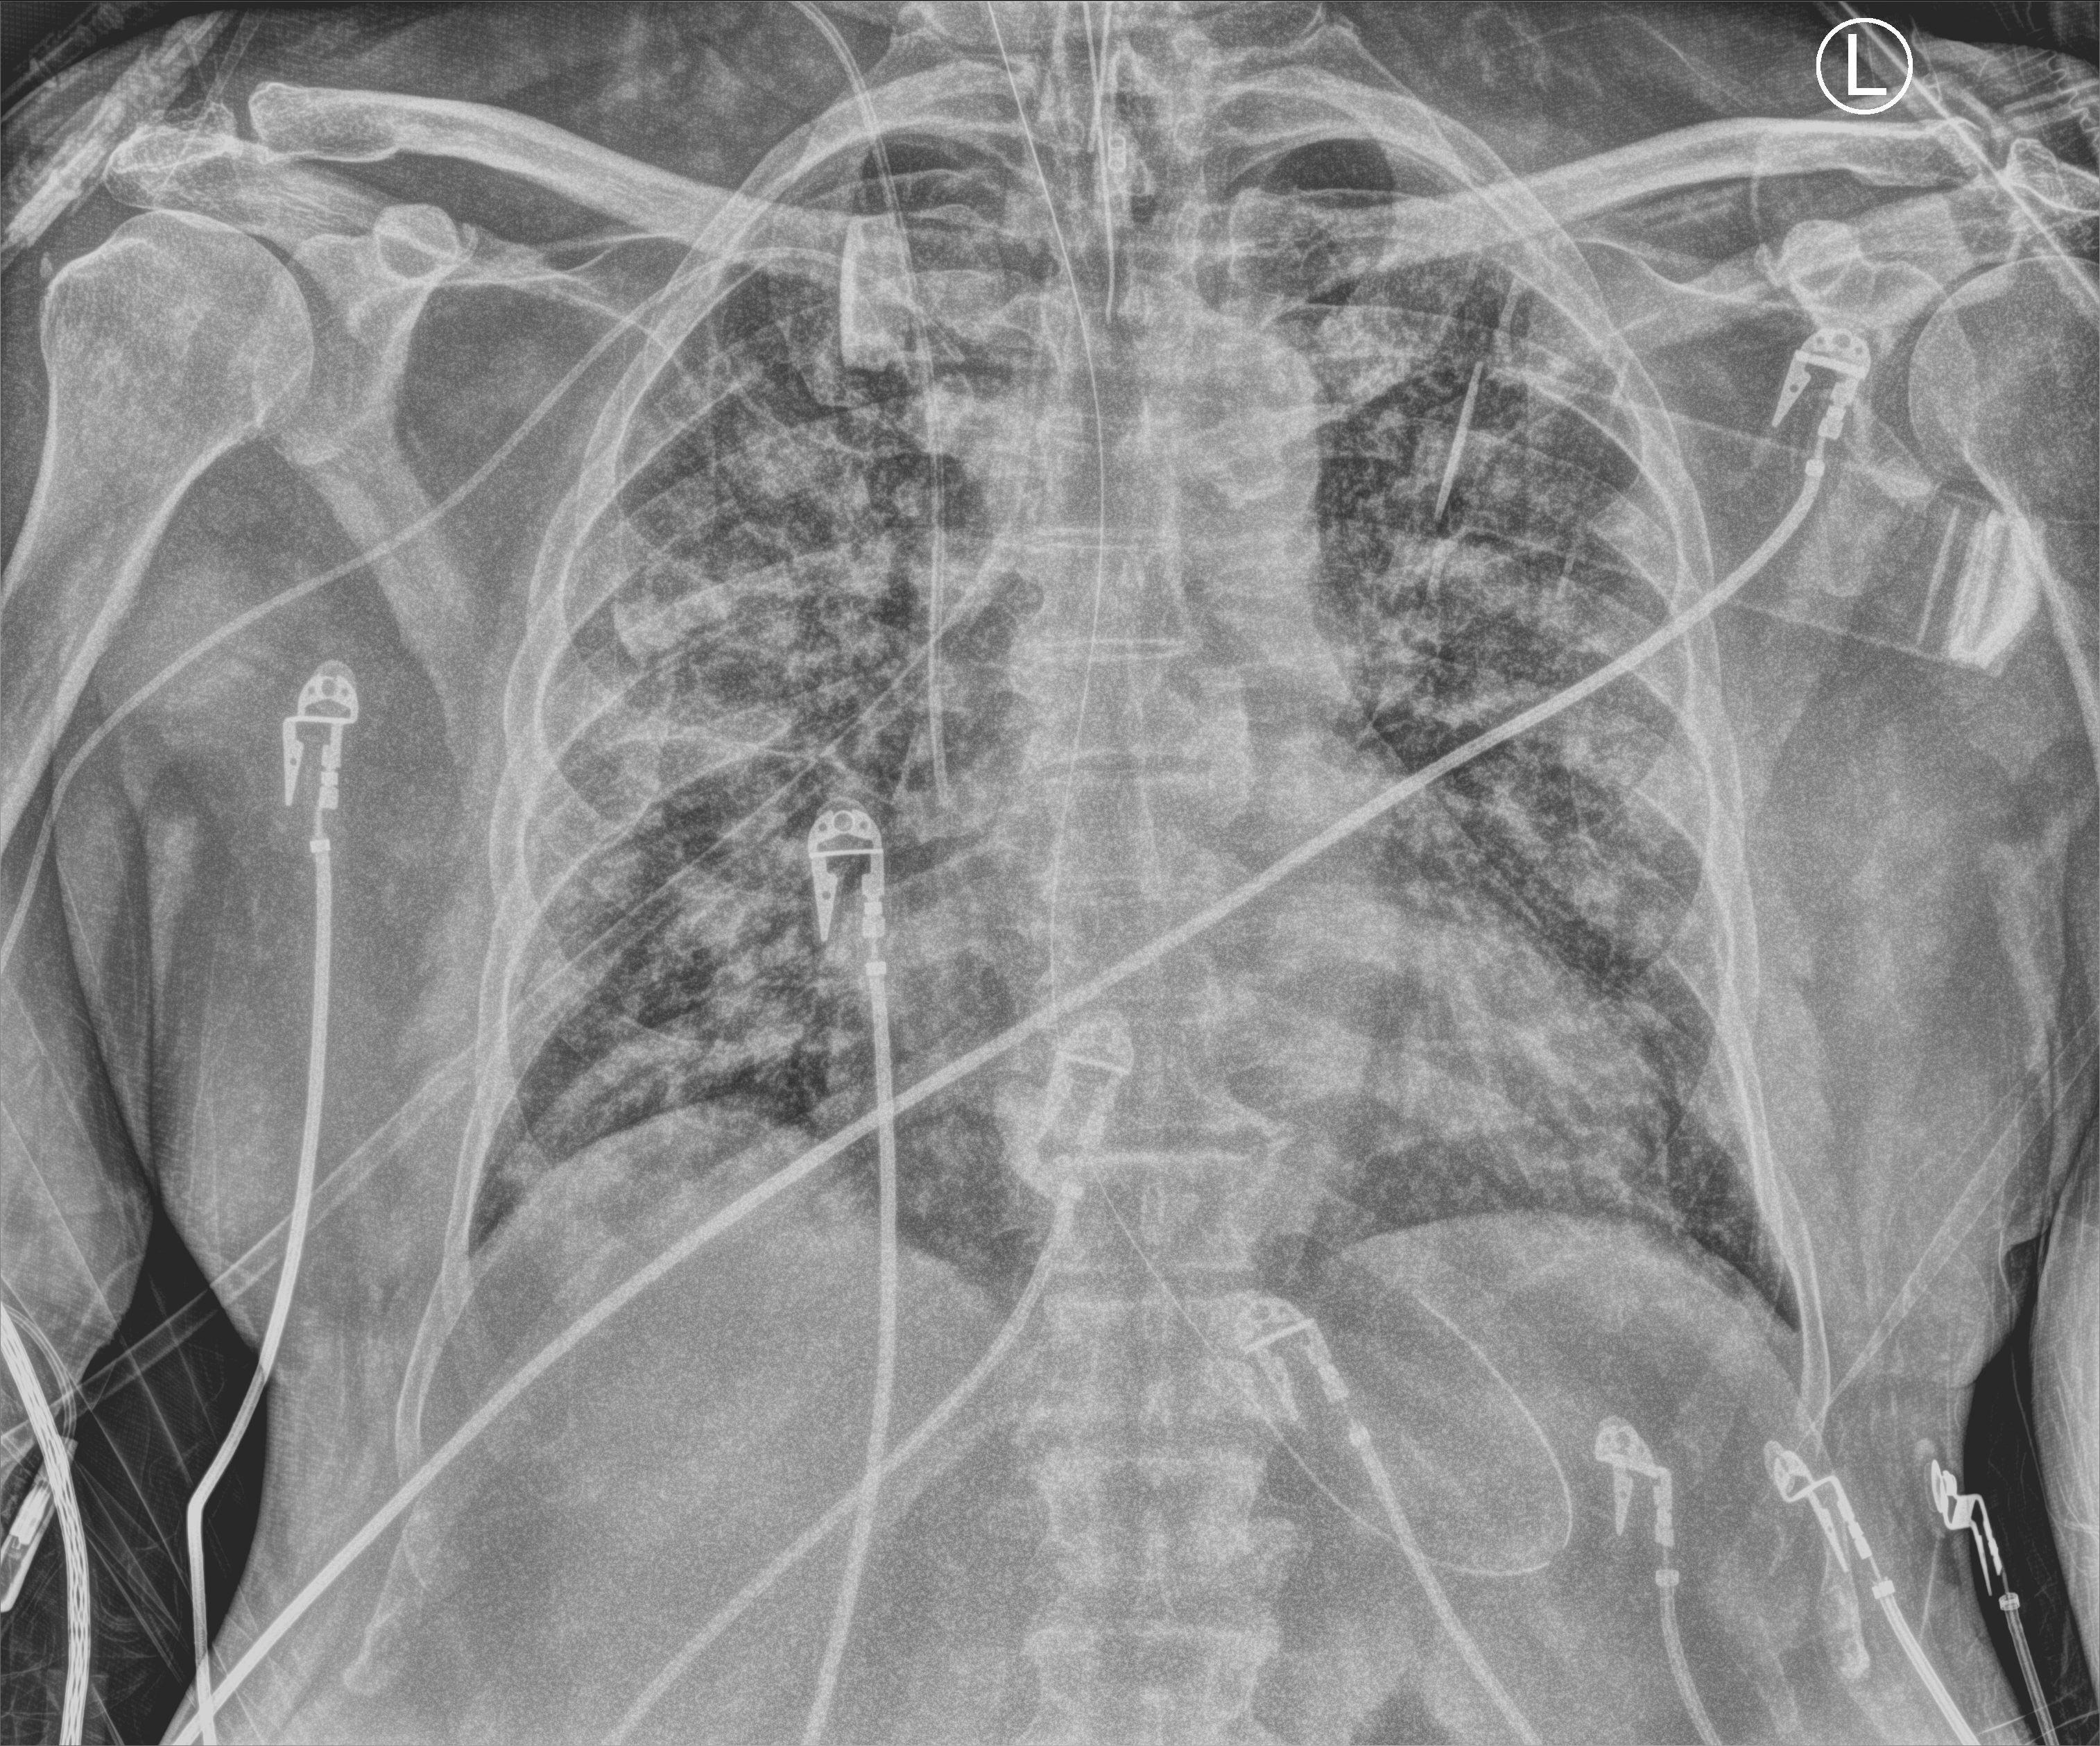
Bedside chest radiograph (computed radiography). Male patient hospitalised with COVID-19, age 60–74 years.
Admission-level facts for this patient (not findings on this image; timing relative to this image not recorded): mechanically ventilated during this hospital stay: yes.